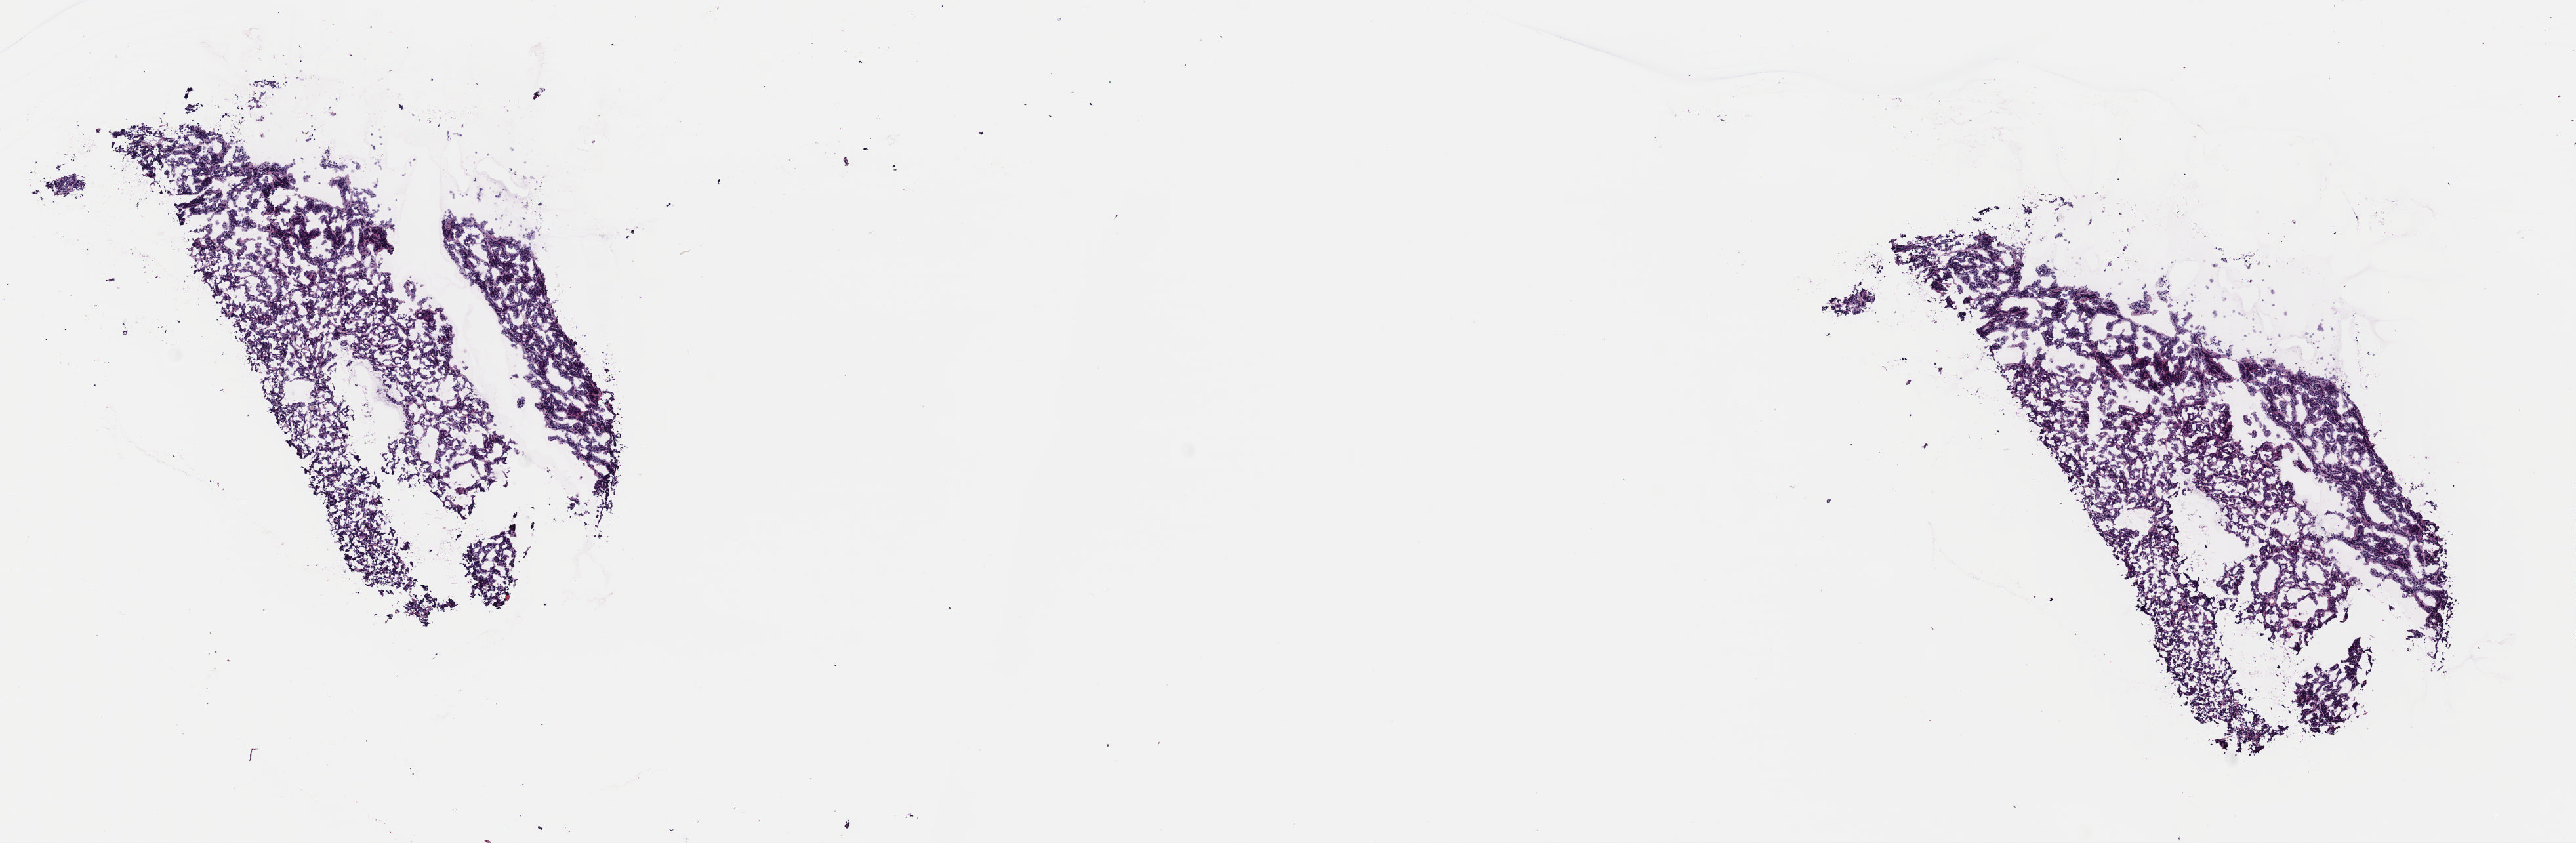
Whole-slide histology image, Hematoxylin and eosin (H&E) stained, low-resolution overview of the scanned area, about 15.5 x 5.1 mm (from a 40x scan), frozen section from the top of the tissue portion, sample: primary tumour, thyroid. Female, age 46 years at initial diagnosis. Pathologist review of this section (percent, as recorded): tumour cells 100%, tumour nuclei 95%, normal cells 0%, stromal cells 0%, necrosis 0%. Infiltration values recorded for this section: lymphocyte infiltration 0%, monocyte infiltration 0%, neutrophil infiltration 0%.
* AJCC pathologic stage: II (6th edition)
* pathologic diagnosis: Papillary adenocarcinoma, NOS (thyroid gland)